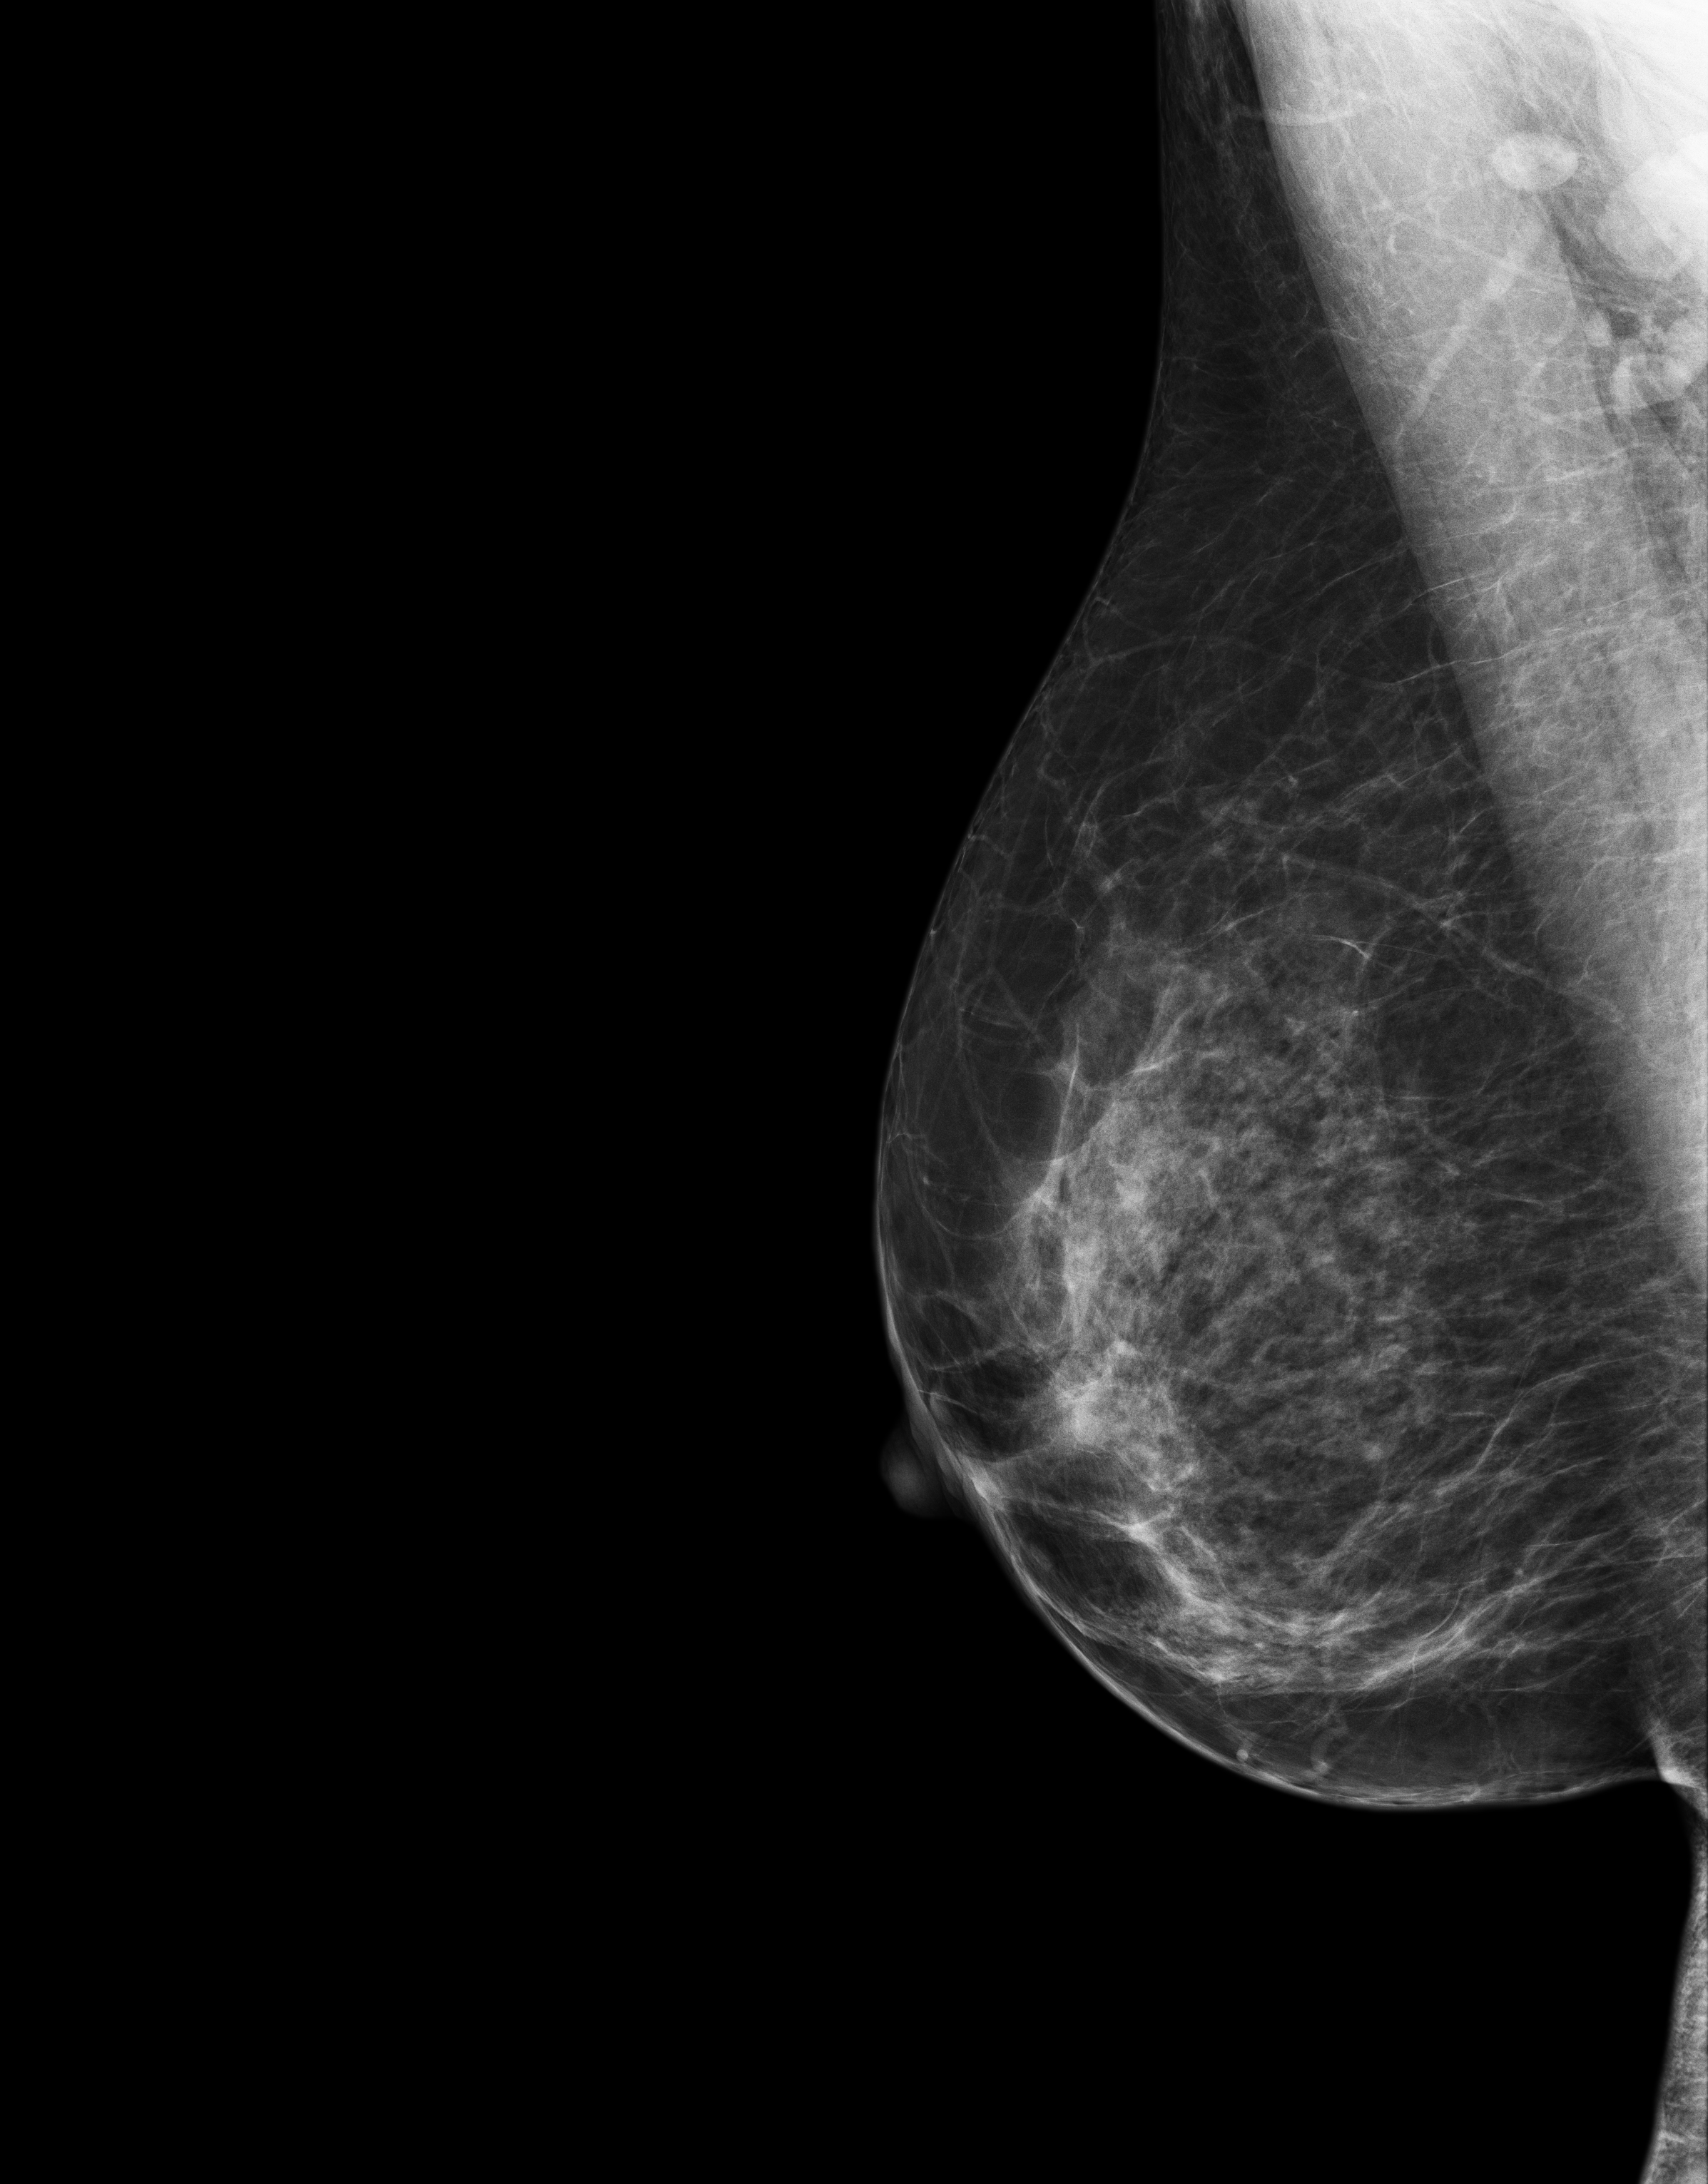
Annual screening mammography examination, compressed breast thickness 55 mm, system: Senographe Essential ADS_56.21.3. Patient: female, 54 years.
Image type: full-field digital mammogram. Breast: right. Projection: medio-lateral oblique projection.